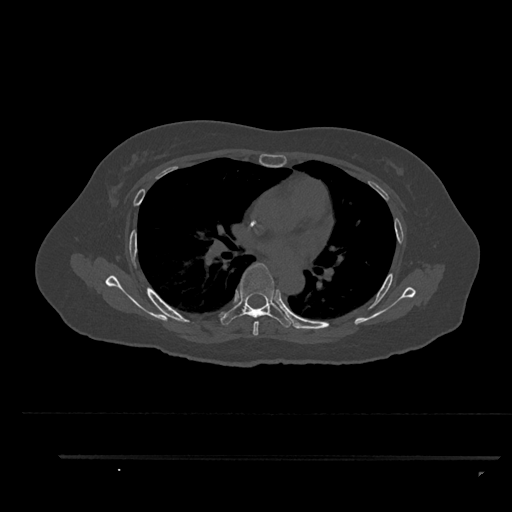
CT including the spine, one axial slice; slice 569 of 797 in the series (ordered by position); reconstruction kernel Br40s/3; bone window (W 1800 / L 400 HU); 512 × 512 image matrix, field of view 408 × 408 mm. Female patient, age 44 years. Case-level facts recorded for this patient, not image findings: primary cancer: renal.
Annotated regions visible in this slice (semi-automatic segmentation, software-assisted and operator-edited):
- T5 vertebra: bounding box <253,321,259,336> (left, top, right, bottom; pixels)
- T6 vertebra: <220,263,293,328>